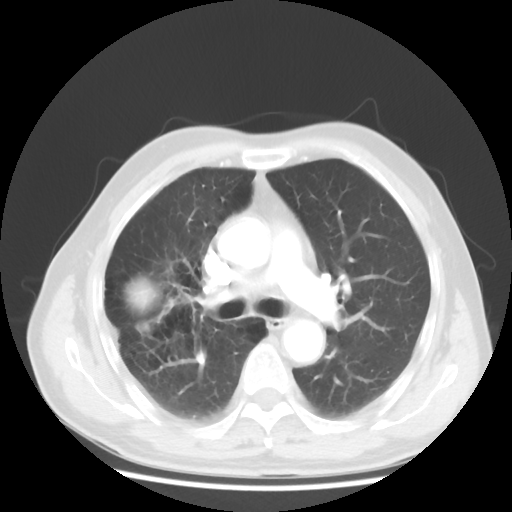
Chest CT, one axial slice. Slice 30 of 50 in the series (ordered by position). Lung window (W 1500 / L -600 HU). 5 mm slice thickness. 512 × 512 image matrix, field of view 360 × 360 mm. Male patient, age 69 years. From the clinical record (not read from this slice): clinical TNM (as recorded): T3 N0 M0.
Structures marked on this image (bounding box drawn by a radiologist):
- lung tumour (recorded histology: adenocarcinoma): box from (x=120, y=271) to (x=165, y=317) px